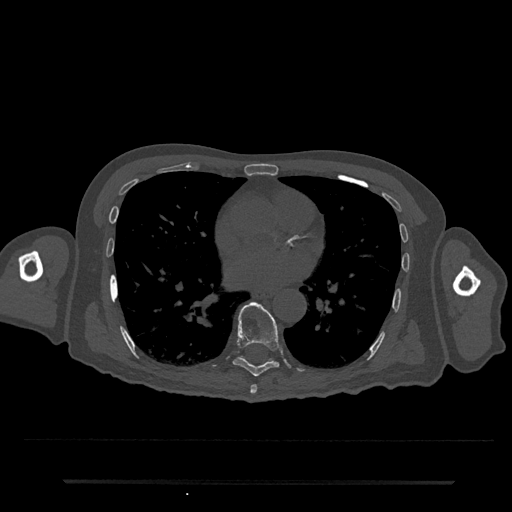
CT including the spine, one axial slice; slice 416 of 797 in the series (ordered by position); 120 kVp; bone window (W 1800 / L 400 HU); 0.5 mm slice thickness; 512 × 512 image matrix, field of view 427 × 427 mm. Patient: male, 74 years. From the clinical record (not read from this slice): primary cancer: prostate.
Annotated regions visible in this slice (semi-automatic segmentation, software-assisted and operator-edited):
- T7 vertebra: box from (x=250, y=384) to (x=257, y=394) px
- T8 vertebra: (x=233, y=302)–(x=280, y=377)